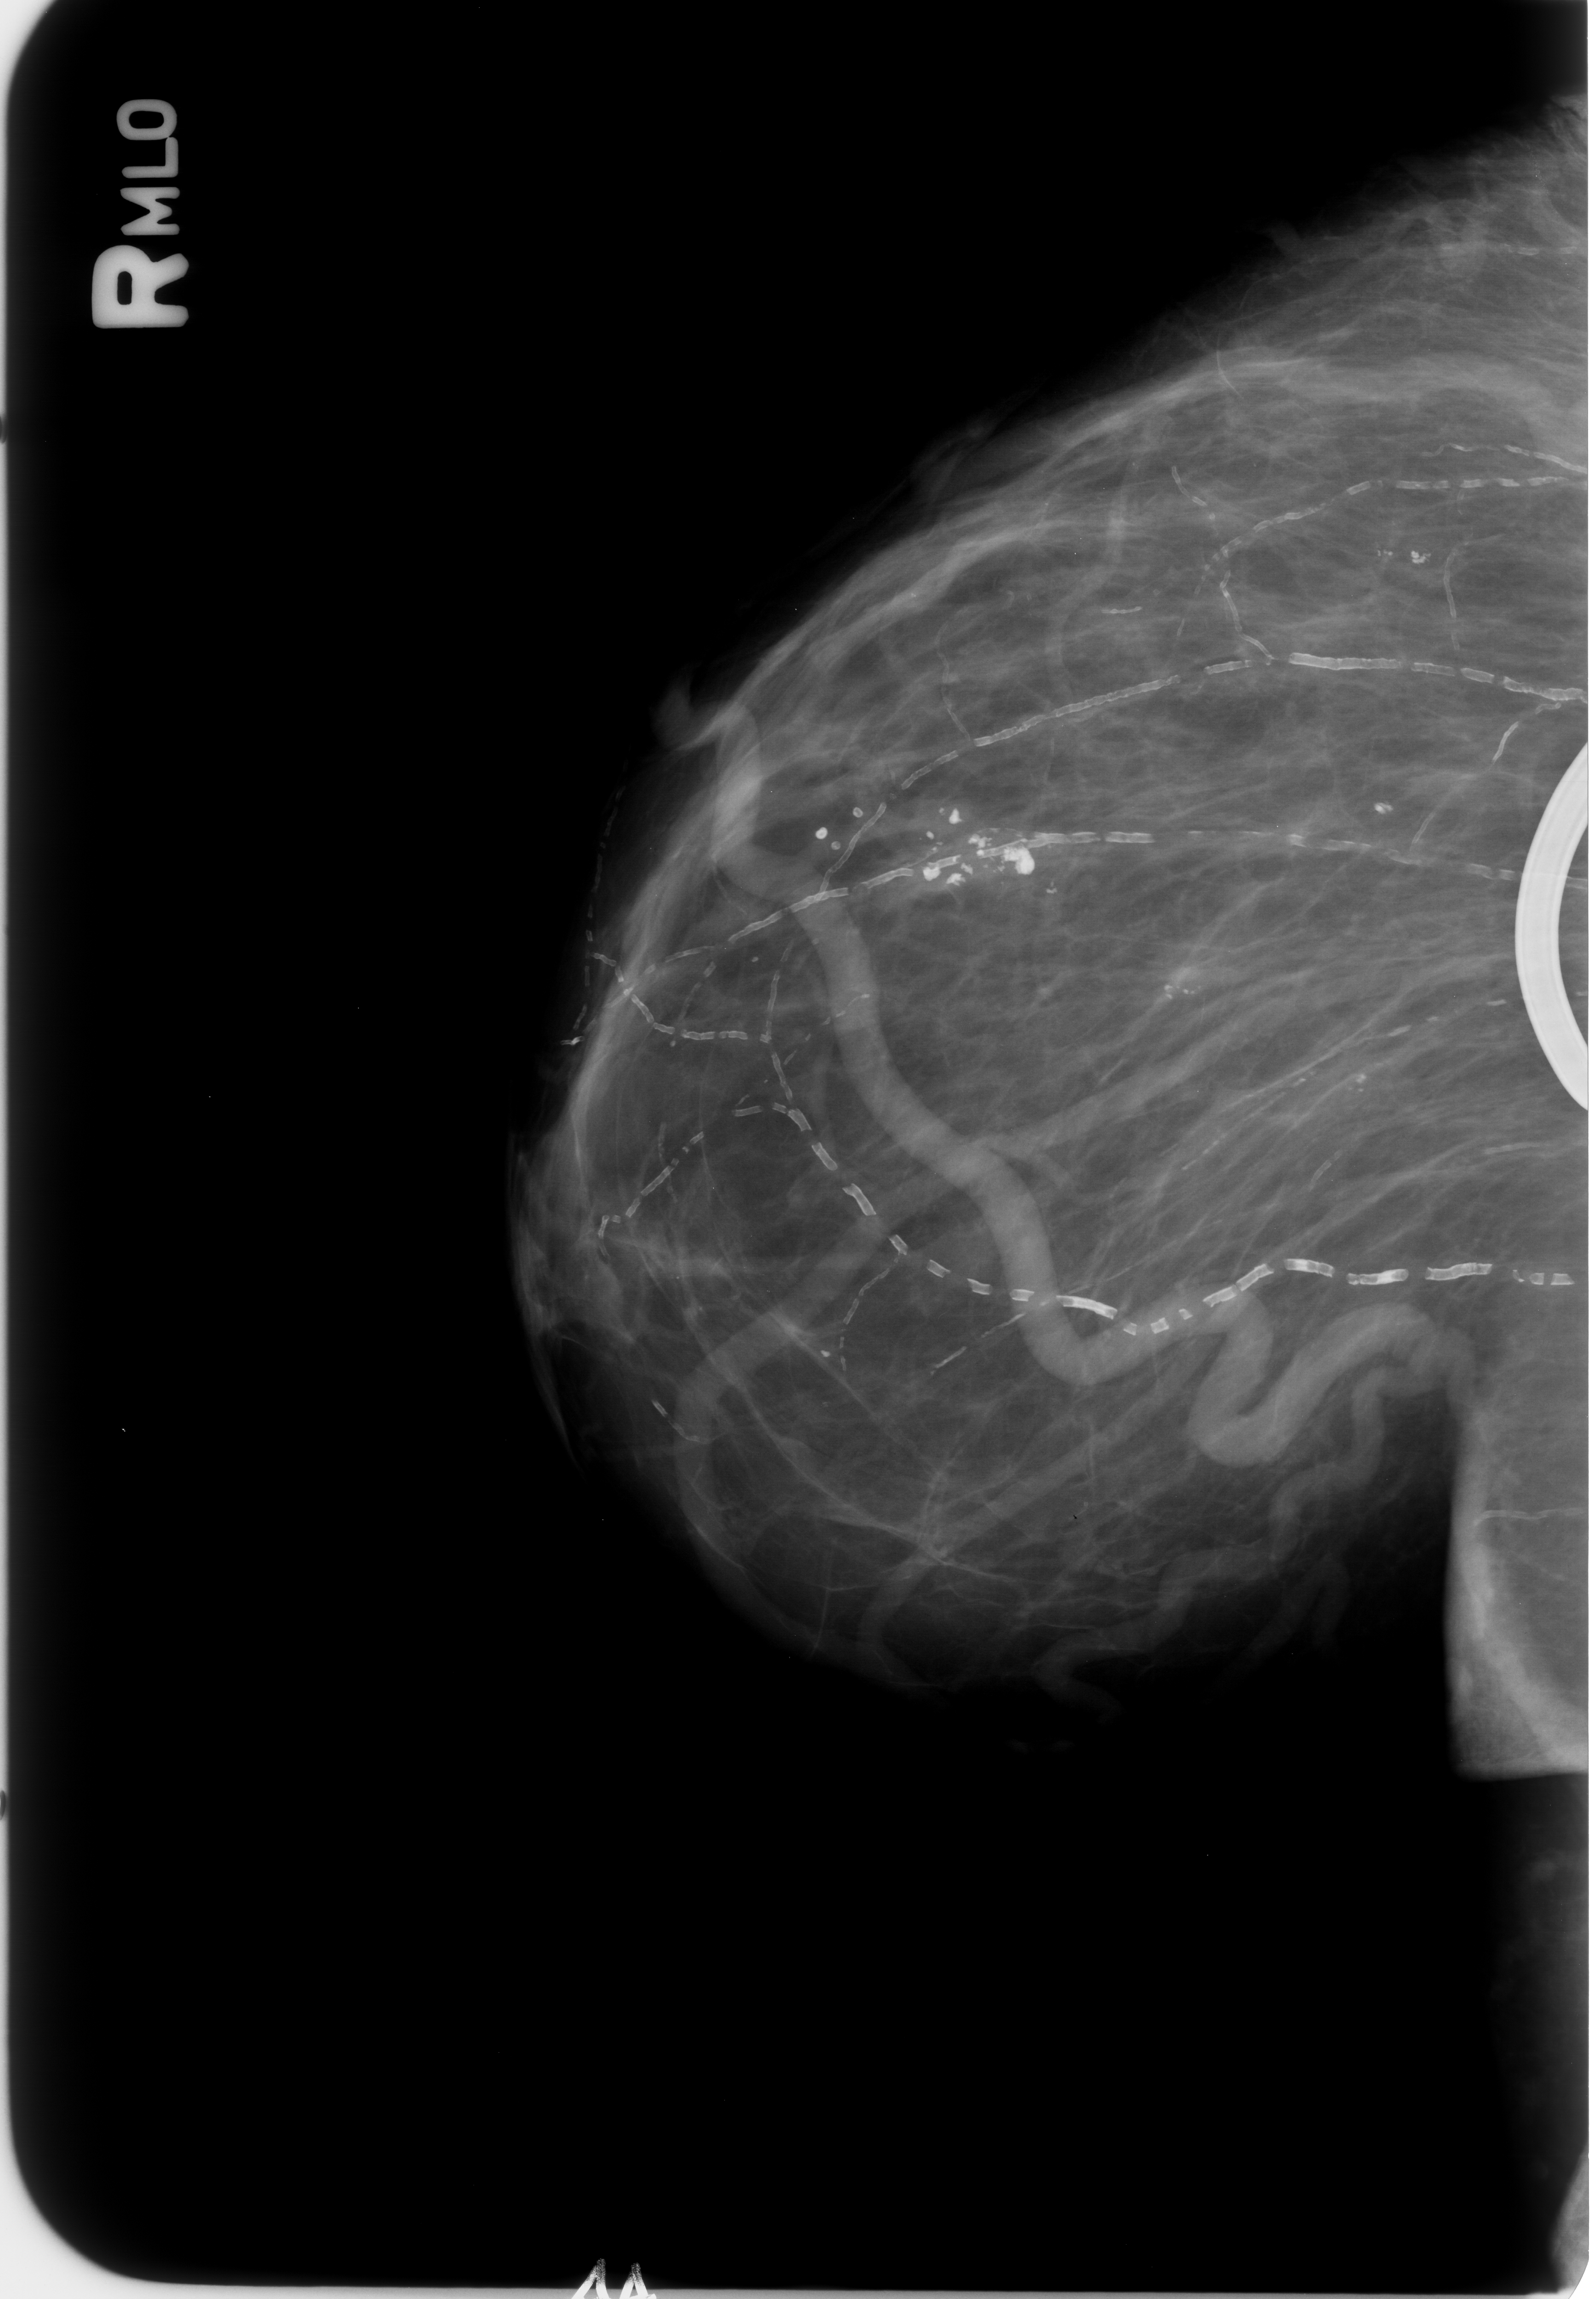
Scanned film-screen mammogram; right breast; mediolateral oblique (MLO) view; breast composition: almost entirely fatty (BI-RADS density category 1 of 4); 1596 × 2299 image matrix.
Marked abnormalities (boxes around the expert regions of interest):
- calcifications, morphology coarse / pleomorphic, distribution clustered; BI-RADS assessment category 2; subtlety rating 5 on a 1 (subtle) to 5 (obvious) scale; pathology (as recorded): benign: bounding box [x1, y1, x2, y2] px = [873, 760, 1019, 926]